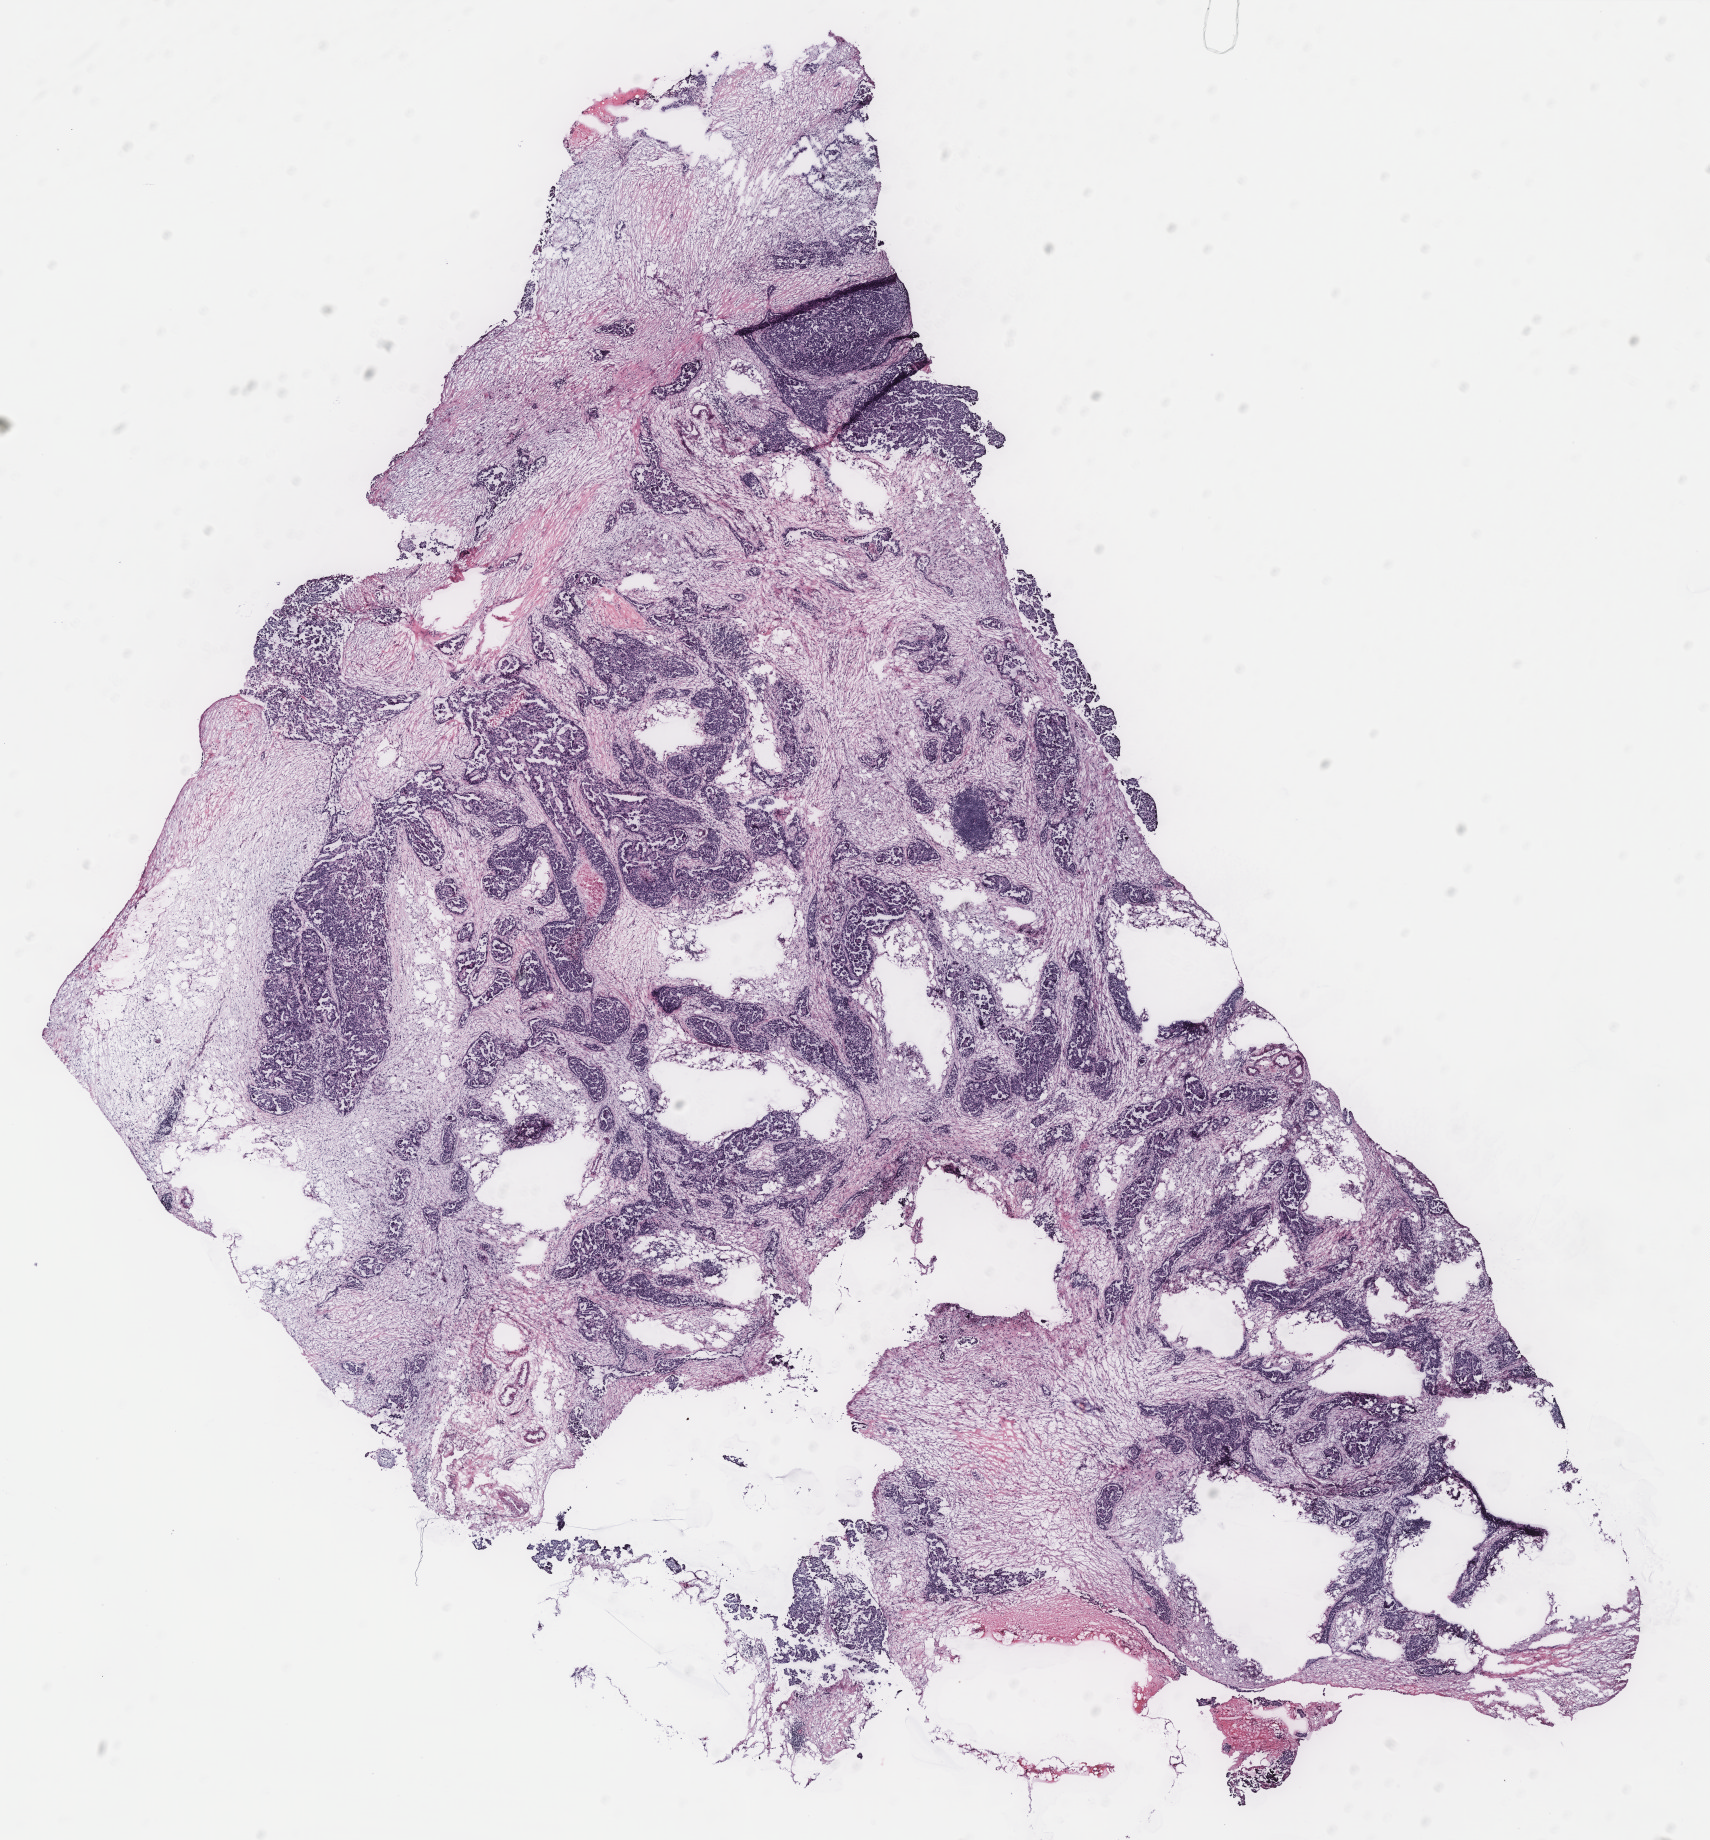
Whole-slide histology image, Hematoxylin and eosin (H&E) stained — whole scanned area (about 13.7 x 14.7 mm, slide scanned at 40x) shown as a low-resolution overview. Ovary, tumour tissue. Patient: female, age 77 years.
Histologic diagnosis: Serous adenocarcinoma, NOS (peritoneum, NOS).